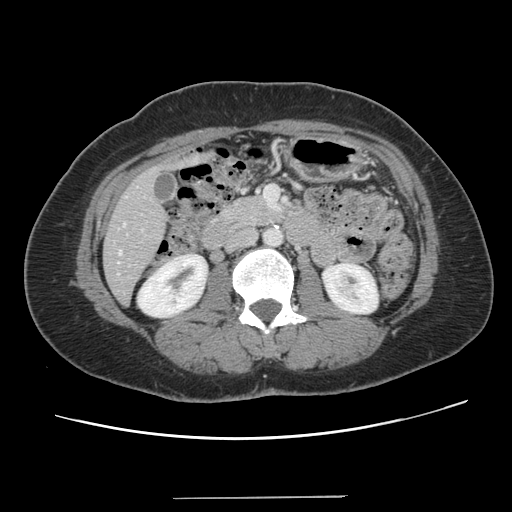
Contrast-enhanced abdominal CT, one axial slice; intravenous contrast given; soft-tissue window (W 400 / L 40 HU); 2.5 mm slice thickness; 512 × 512 image matrix, field of view 366 × 366 mm. Female patient, age 53 years. Case-level facts recorded for this patient, not image findings: diagnosis: colorectal cancer liver metastases, imaged before liver resection; multiple liver metastases: no; largest metastasis: 14.5 cm; disease in both lobes: yes.
Outlined on this slice (outlined manually by an expert reader):
- hepatic veins: bounding box (x1, y1, x2, y2) in pixels: (118, 251, 121, 254)
- liver: (104, 157, 202, 303)
- planned liver remnant (the part of the liver to remain after resection): (104, 217, 166, 303)